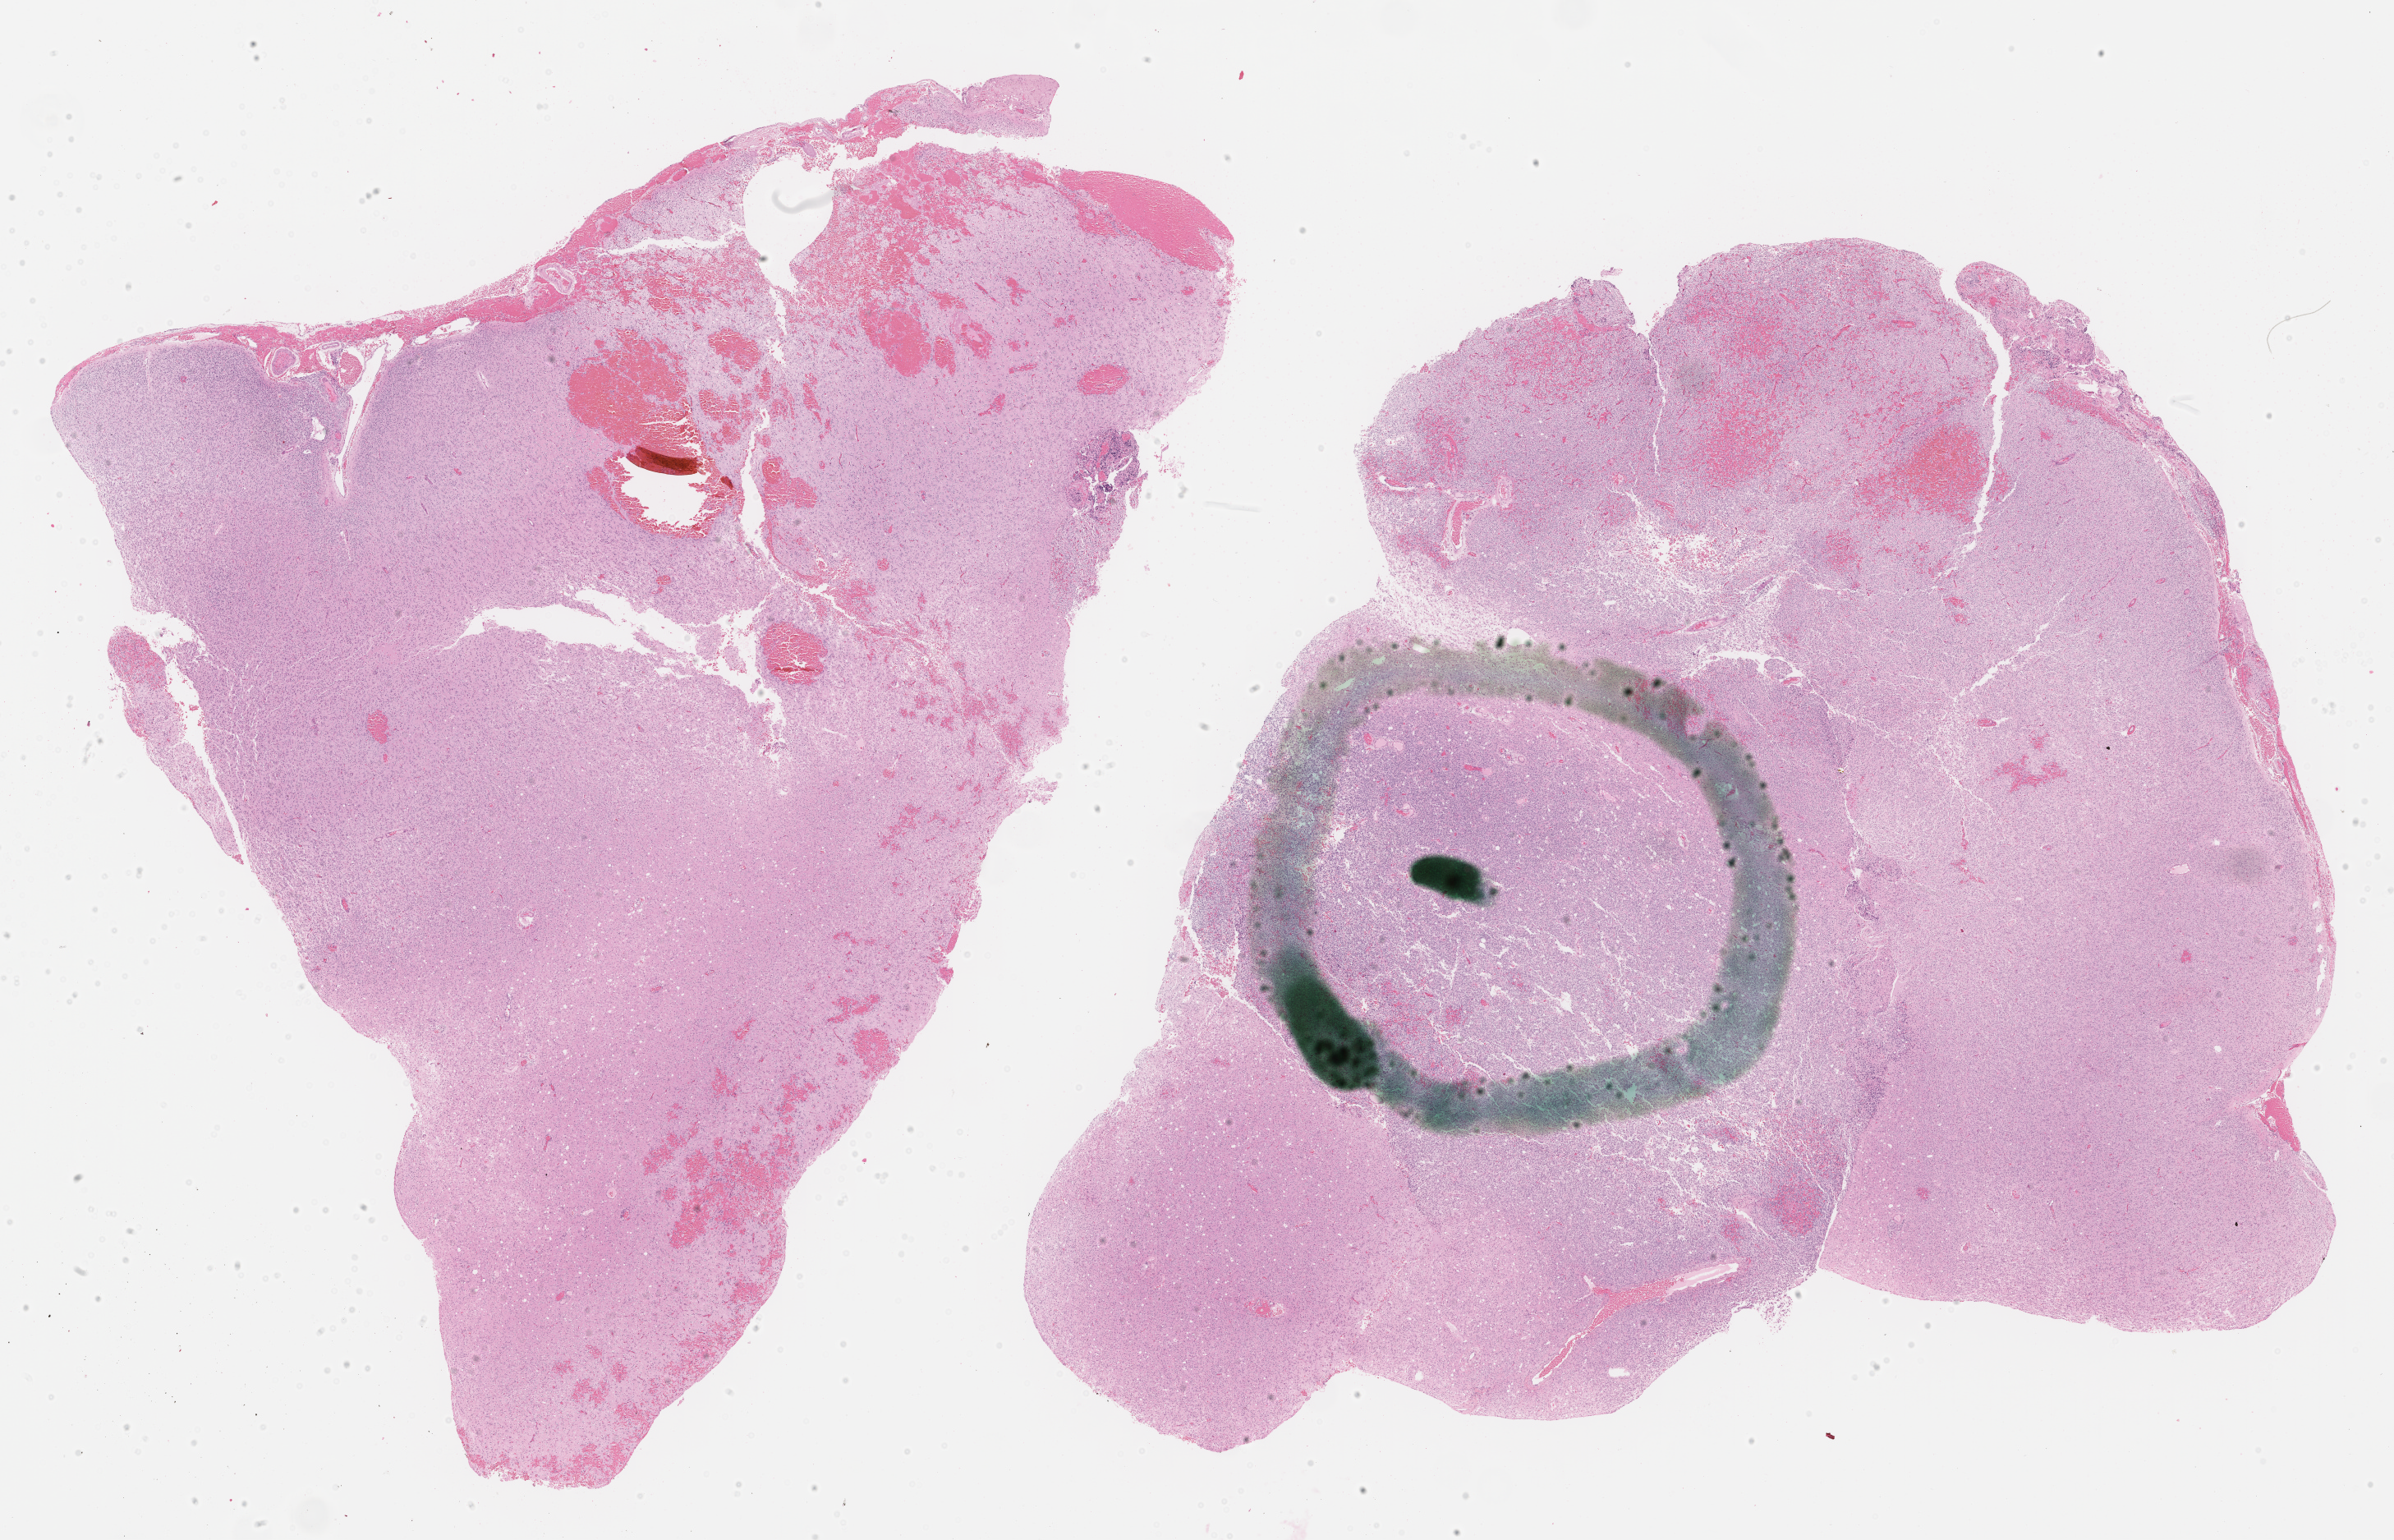
Whole-slide histology image, Hematoxylin and eosin (H&E) stained, whole scanned area (about 23.5 x 15.1 mm, from a 40x scan) shown as a low-resolution overview. FFPE section. Sample: primary tumour, brain. Male patient; age at initial diagnosis 52 years.
Histologic diagnosis: Oligodendroglioma, anaplastic (cerebrum).